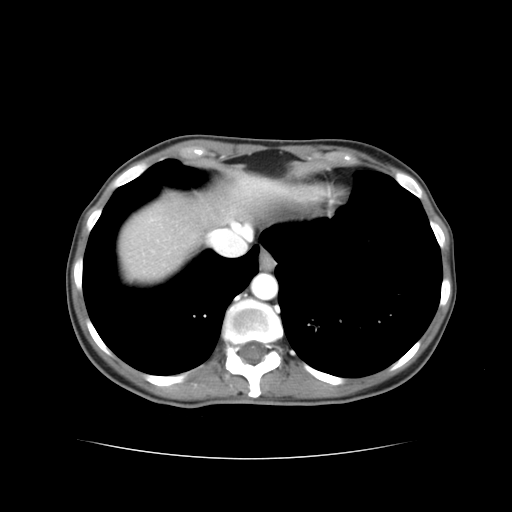
Contrast-enhanced abdominal CT, one axial slice; position 35 of 38 along the scan axis; reconstruction kernel STANDARD; 120 kVp; soft-tissue window (W 400 / L 40 HU); 5 mm slice thickness; 512 × 512 image matrix. Female patient, age 54 years. From the clinical record (not read from this slice): diagnosis: colorectal cancer liver metastases, imaged before liver resection; multiple liver metastases: yes; largest metastasis: 1.1 cm; disease in both lobes: yes.
Outlined on this slice (expert manual segmentation):
- hepatic veins: bounding box <215,231,225,238> (left, top, right, bottom; pixels)
- liver: <122,178,296,275>
- planned liver remnant (the part of the liver to remain after resection): <217,178,296,215>